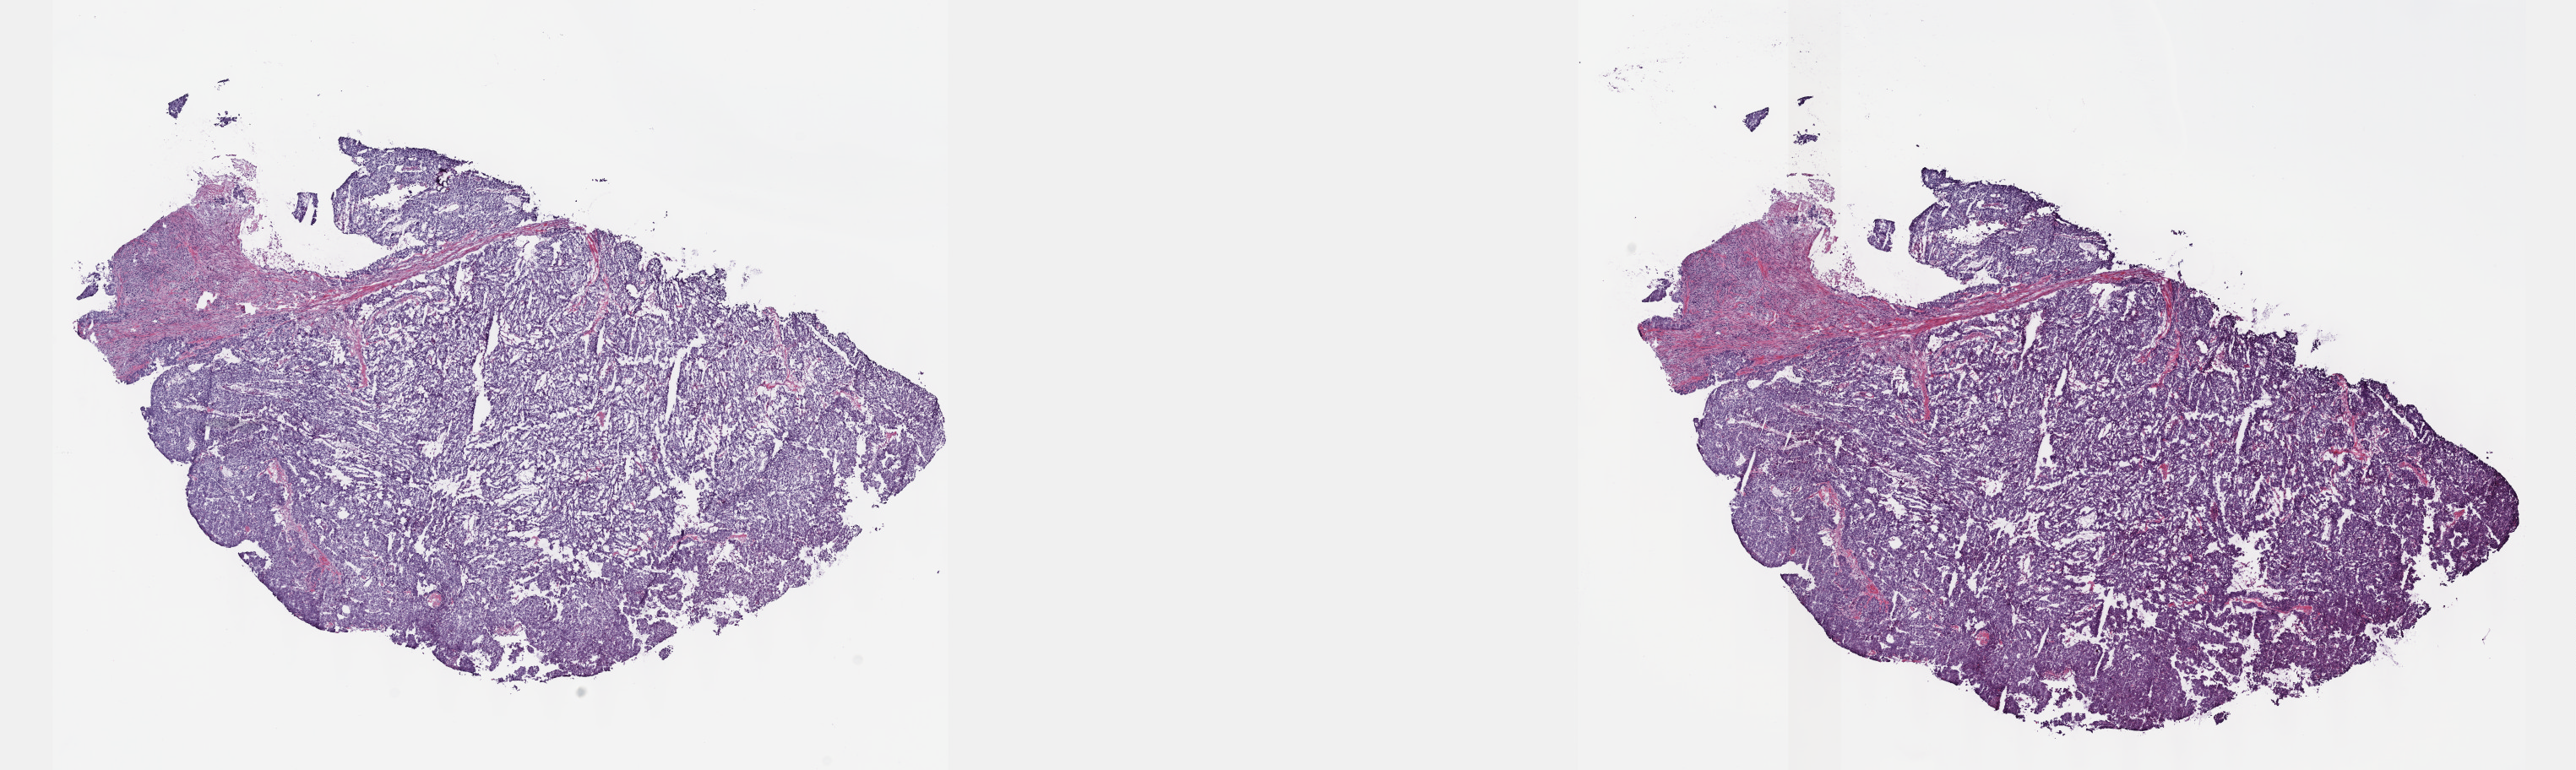
Whole-slide histology image, H&E-stained, low-resolution overview of the scanned area, about 24.6 x 7.4 mm (acquisition: 40x scan), frozen section from the top of the tissue portion, primary tumour sample from the testis. Male, age 38 years at initial diagnosis. Composition of this section per pathologist review: tumour cells 80%, tumour nuclei 80%, normal cells 0%, stromal cells 20%, necrosis 0%. Inflammatory infiltration, as recorded: lymphocyte infiltration 3%, monocyte infiltration 1%, neutrophil infiltration 2%.
Histologic diagnosis: Embryonal carcinoma, NOS. AJCC pathologic stage: IIA (6th edition).